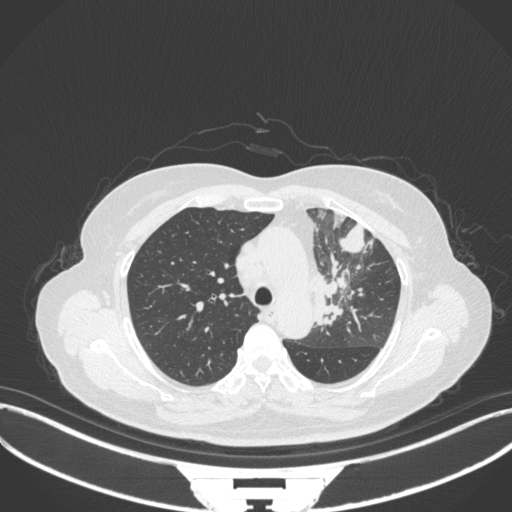
Chest CT, one axial slice; position 242 of 382 along the scan axis; 120 kVp; lung window (W 1500 / L -600 HU); 512 × 512 image matrix. Female patient, age 64 years. From the clinical record (not read from this slice): clinical TNM (as recorded): T2a N2 M0.
Annotated regions visible in this slice (rectangle marked by the reading radiologist):
- lung tumour (recorded histology: adenocarcinoma): box from (x=309, y=260) to (x=358, y=331) px
- lung tumour (recorded histology: adenocarcinoma): (x=333, y=221)–(x=369, y=258)